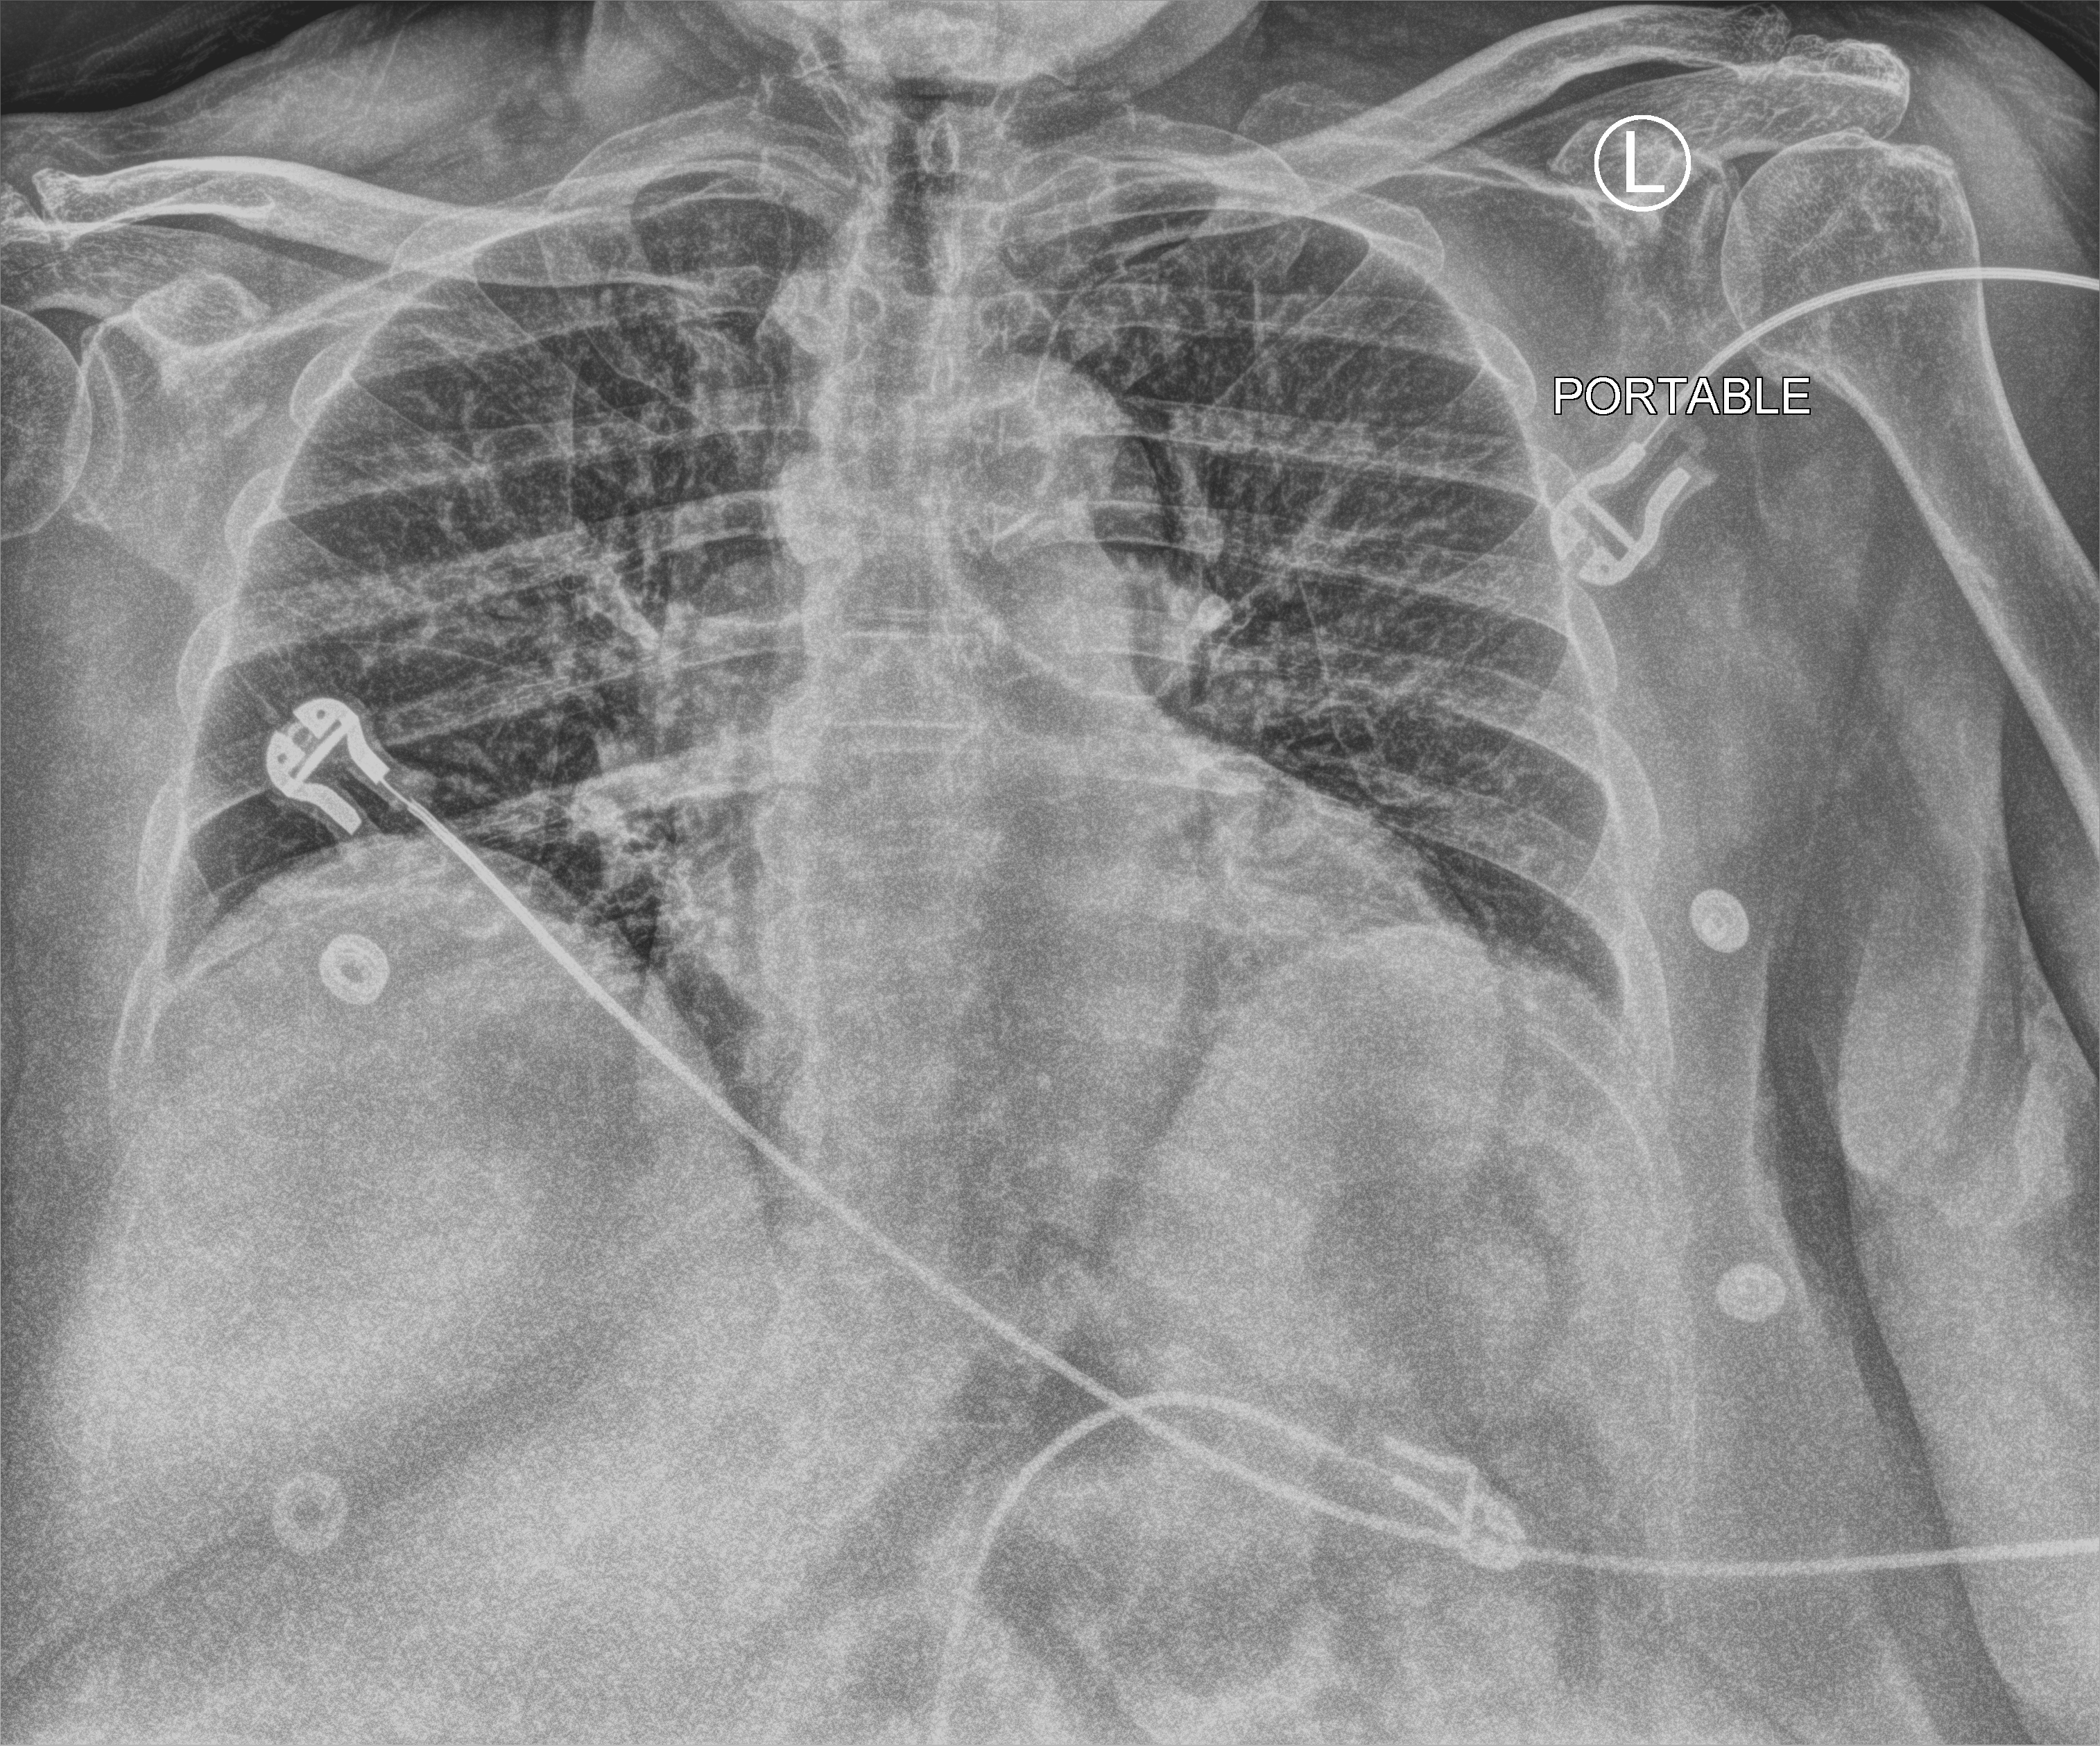
Chest X-ray (portable), anteroposterior (AP) projection. Patient hospitalised with COVID-19; female, aged 75–90 years.
From the hospital-stay record, not from the radiograph (when in the stay this image was taken is not recorded): mechanically ventilated during this hospital stay: no.